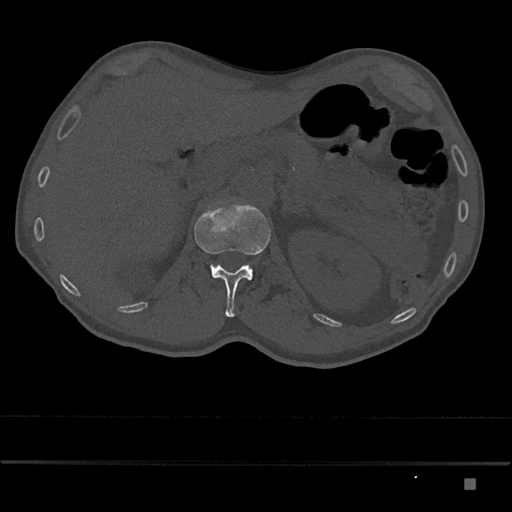
CT including the spine, one axial slice. Slice 538 of 797 in the series (ordered by position). Reconstruction kernel Br40s/3. Bone window (W 1800 / L 400 HU). 0.5 mm slice thickness. 512 × 512 image matrix, field of view 390 × 390 mm. Male patient, age 72 years. From the clinical record (not read from this slice): primary cancer: prostate.
Outlined on this slice (semi-automatically segmented with operator editing):
- L1 vertebra: bounding box <194,205,271,317> (left, top, right, bottom; pixels)